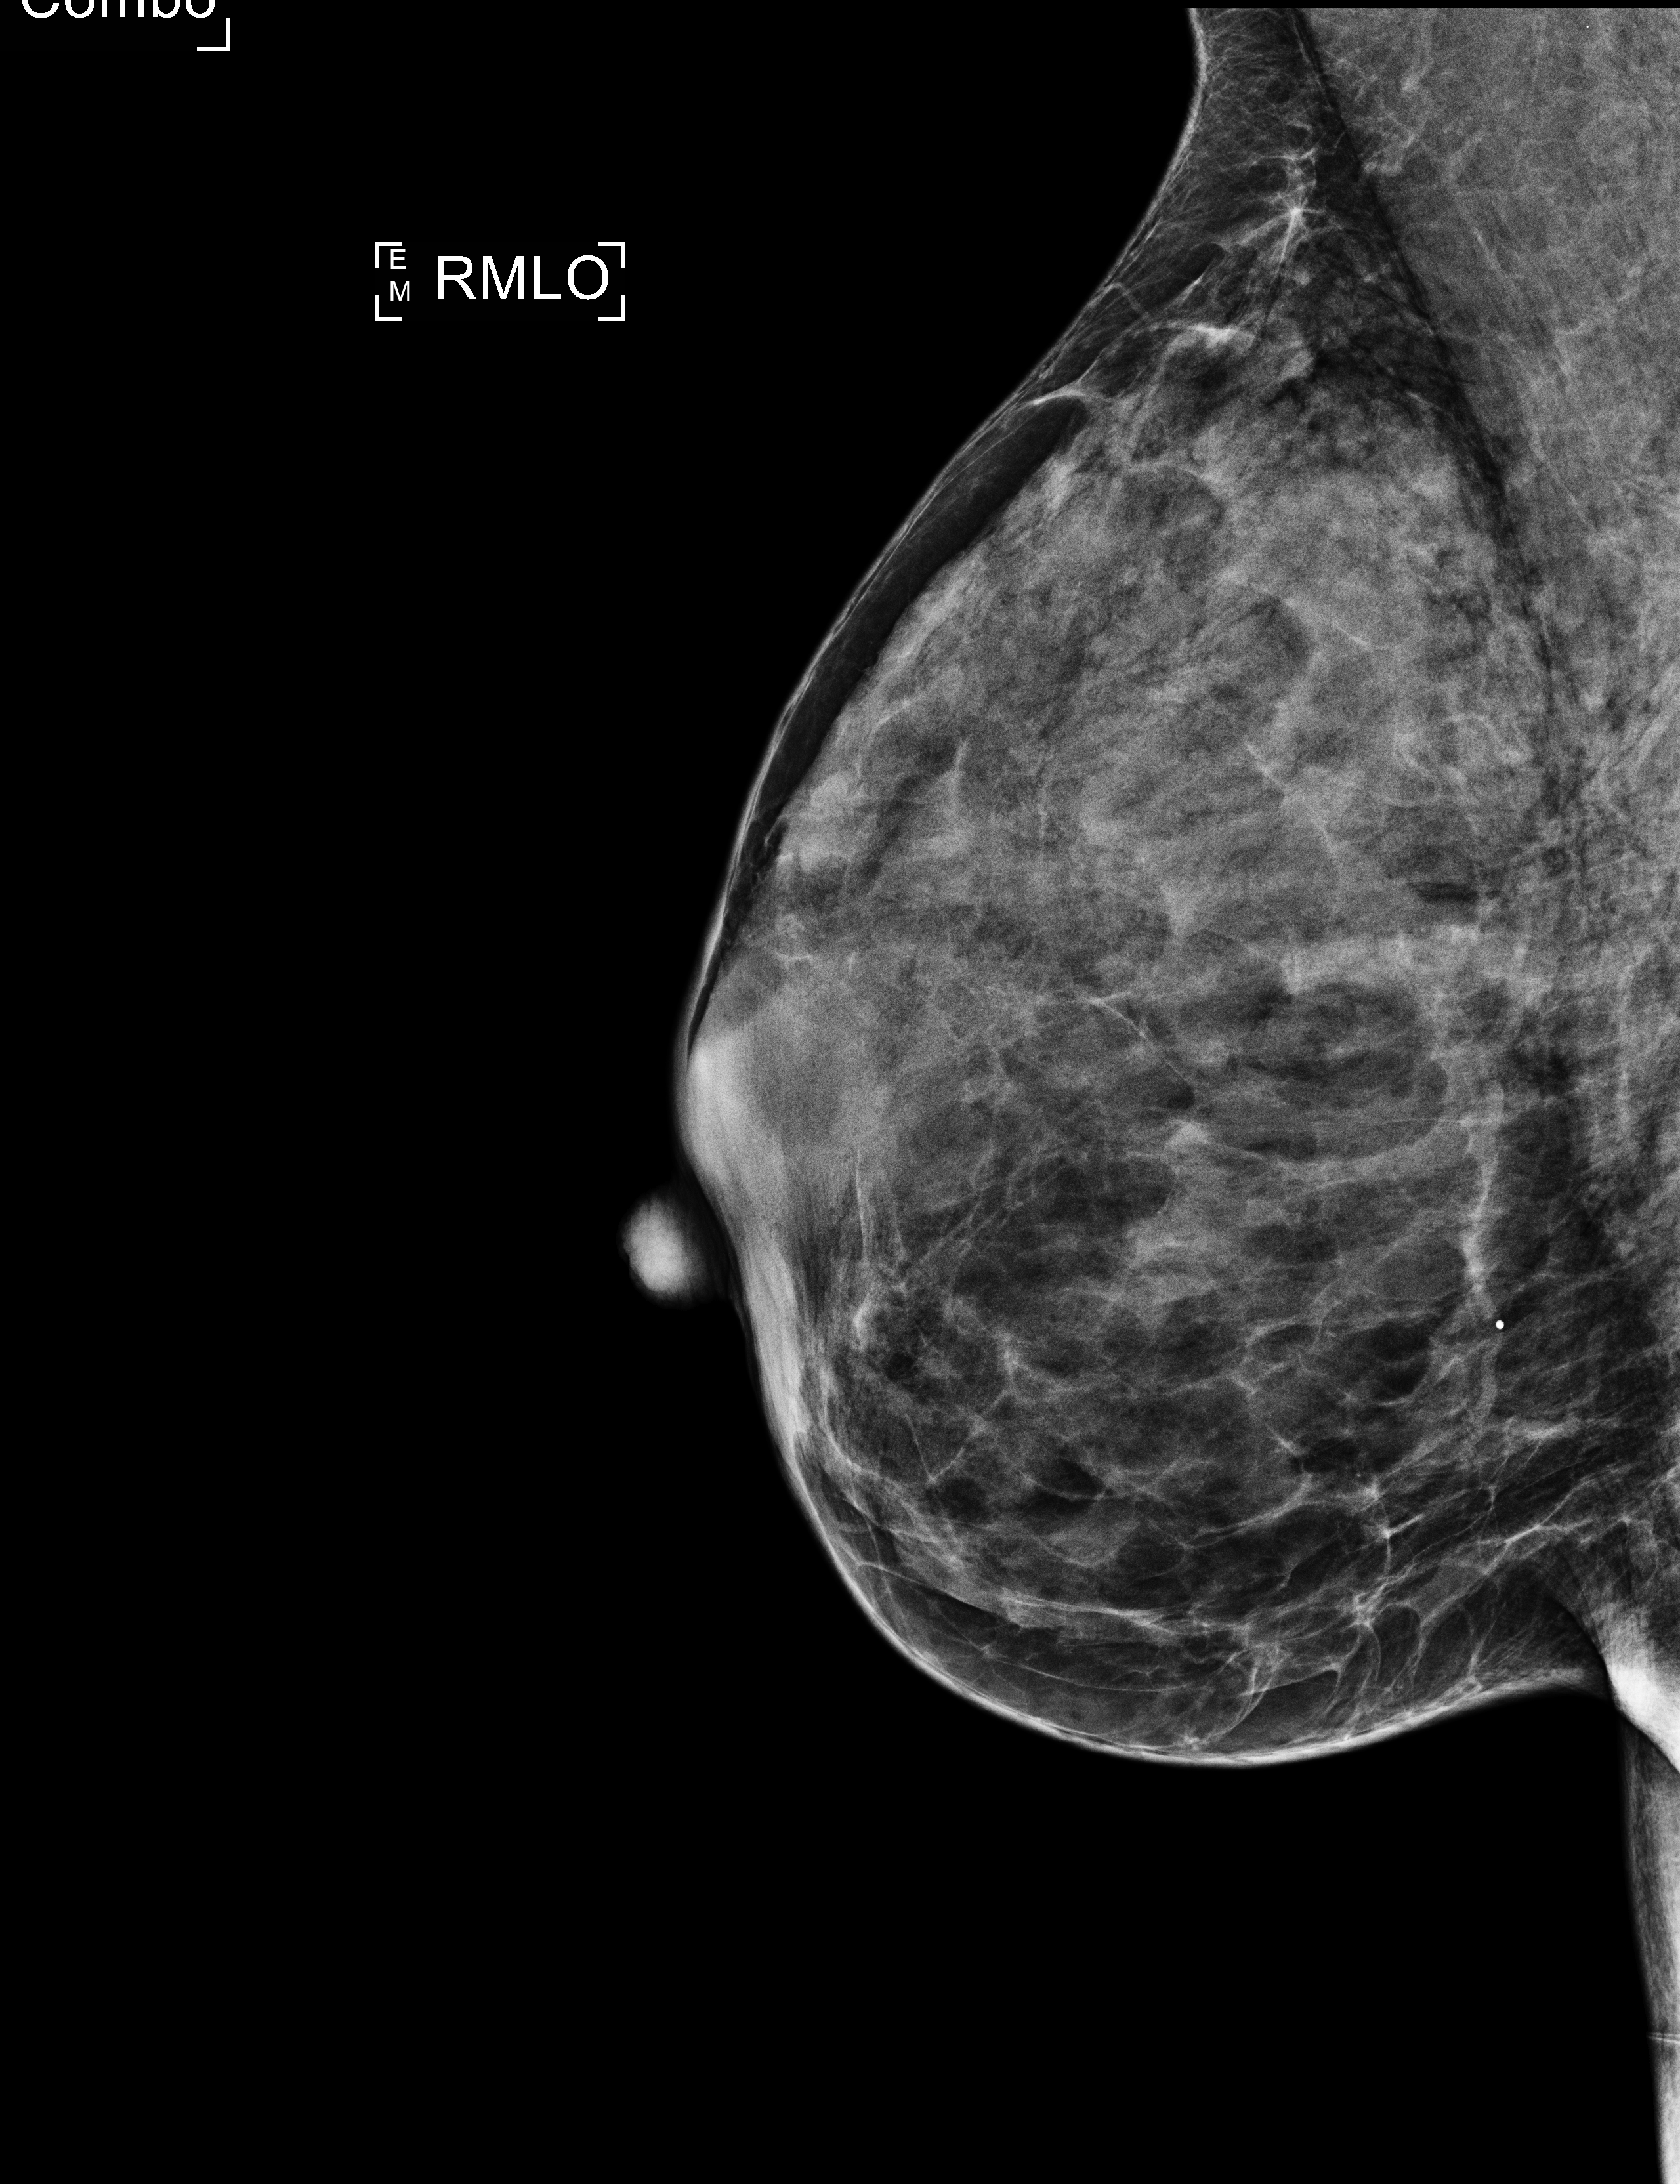
Digital mammogram (FFDM); right breast; medio-lateral oblique projection; screening examination; system: Selenia Dimensions. Patient: female, 55 years.
Breast density at the screening exam (both breasts): extremely dense (BI-RADS density category d). Final BI-RADS assessment for this screening round (tomosynthesis exam, both breasts): category 2. Recall: no recall after this screen.